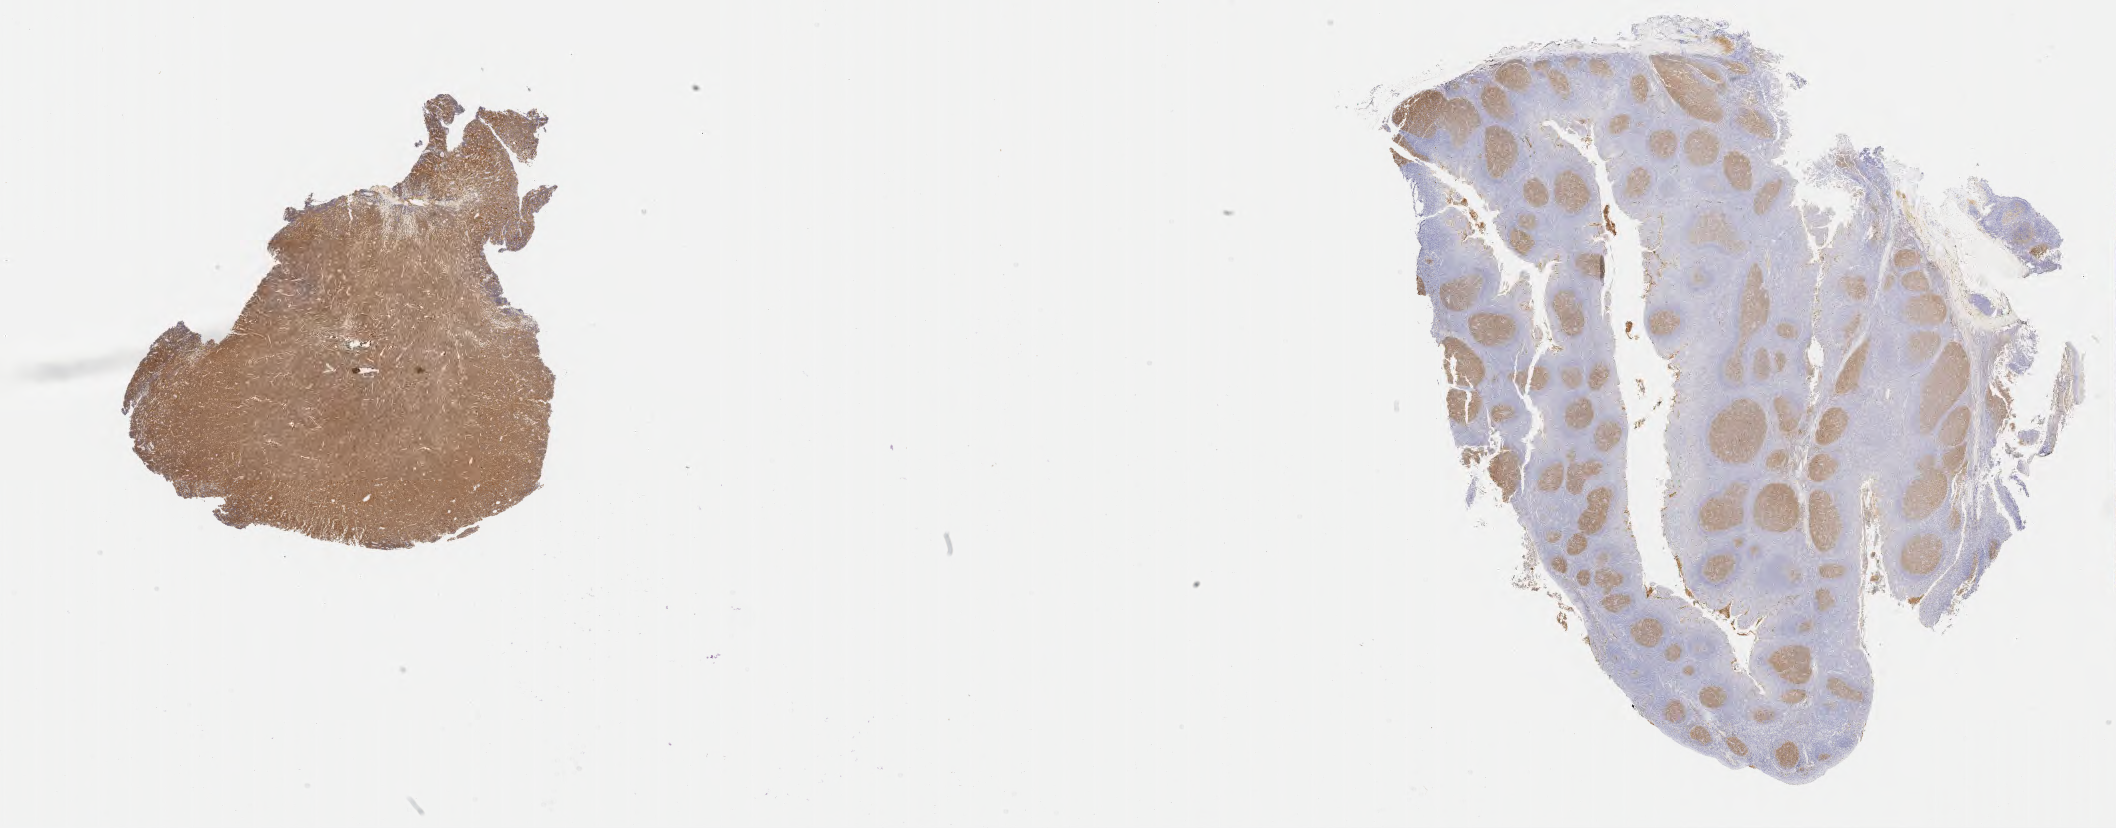
Whole-slide image, immunohistochemical stain for CD10 — a low-resolution overview of the entire scanned area, about 34.2 x 13.4 mm; tumor tissue; anatomic site: mandible. Patient: female, age at initial diagnosis 5 years.
Diagnosis: Burkitt lymphoma, NOS.